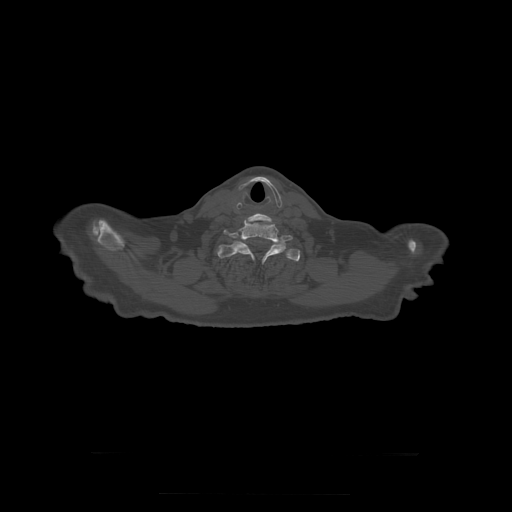
CT including the spine, one axial slice. Position 295 of 397 along the scan axis. 120 kVp. Bone window (W 1800 / L 400 HU). 1.25 mm slice thickness. 512 × 512 image matrix, field of view 510 × 510 mm. Patient age 73 years. From the clinical record (not read from this slice): primary cancer: prostate.
Structures marked on this image (semi-automatically segmented with operator editing):
- T1 vertebra: bounding box <217,241,300,264> (left, top, right, bottom; pixels)